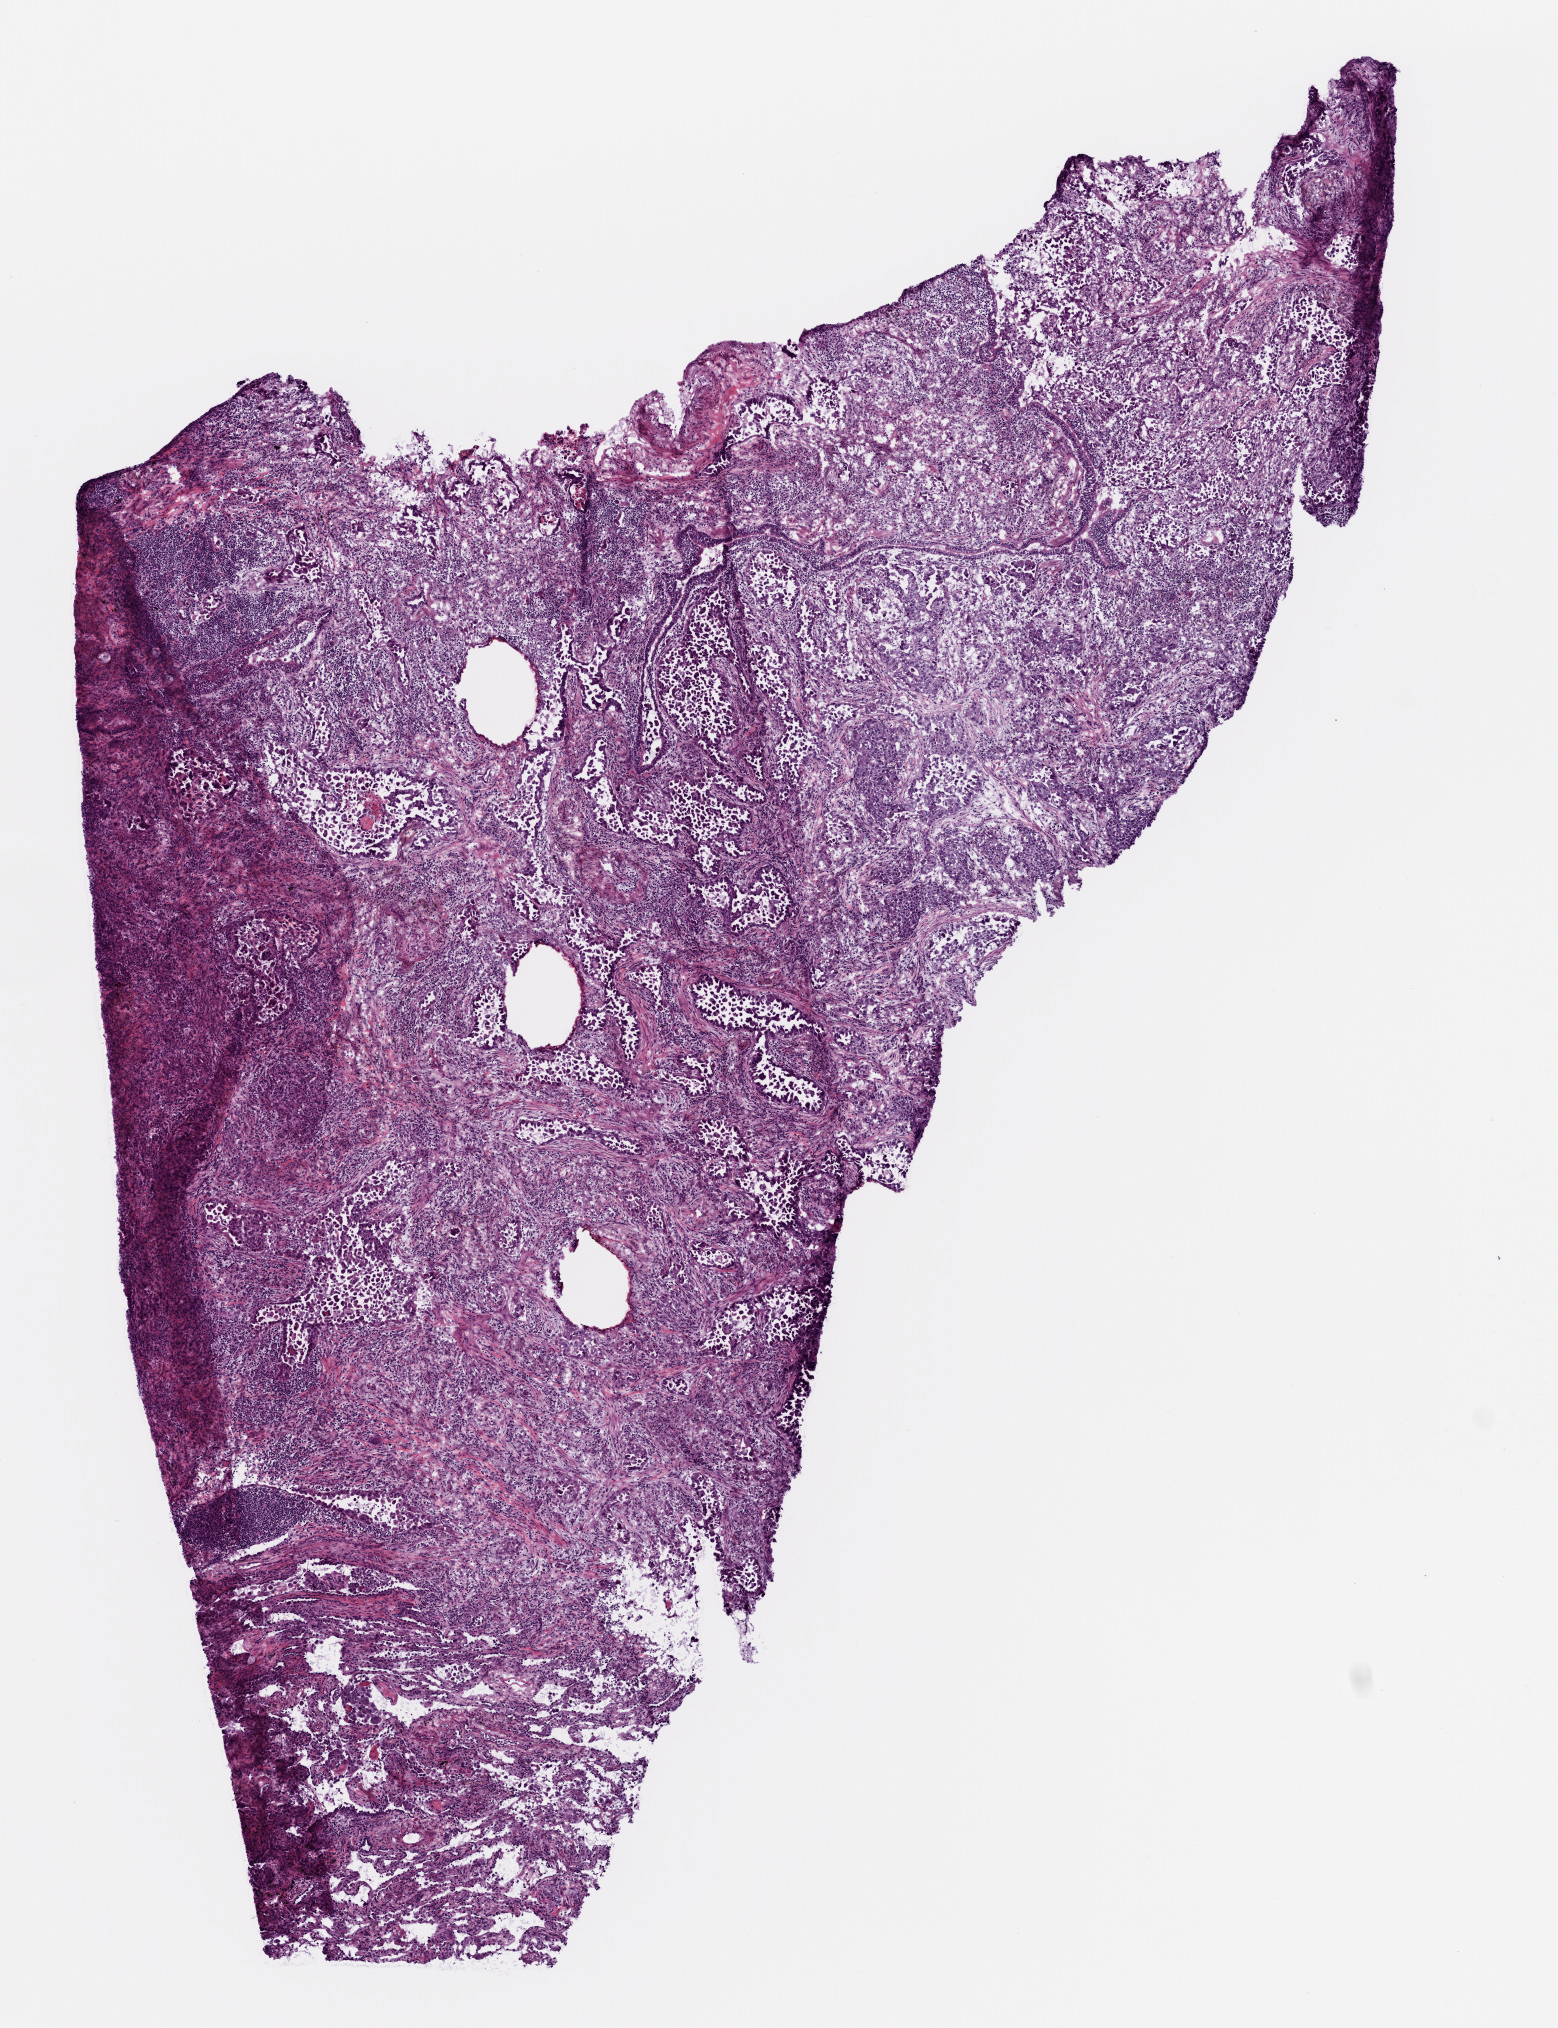
Digitized Hematoxylin and eosin (H&E) stained tissue section (whole slide), shown as a low-resolution overview of the whole scanned area (about 6.3 x 8.2 mm, slide scanned at 20x); frozen section from the top of the tissue portion; lung, primary tumour sample. Patient: male, age at initial diagnosis 77 years. Slide review estimates, as recorded: tumour cells 75%, tumour nuclei 65%, normal cells 0%, stromal cells 25%, necrosis 0%.
Pathologic diagnosis: Adenocarcinoma, NOS. AJCC pathologic stage: IIA (7th edition).